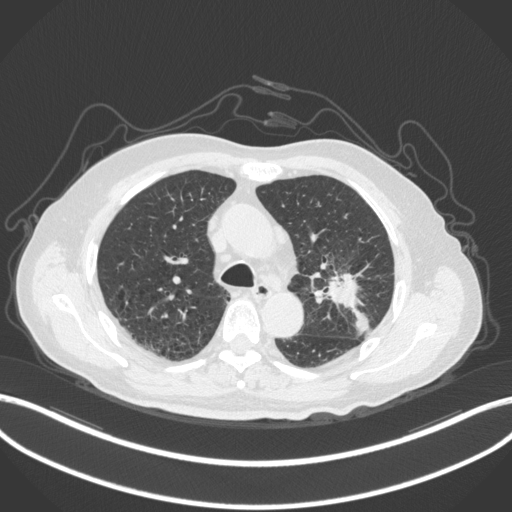
Chest CT, one axial slice; slice 195 of 331 in the series (ordered by position); reconstruction kernel B31f; lung window (W 1500 / L -600 HU); 512 × 512 image matrix, field of view 400 × 400 mm. Patient: male, 79 years. Case-level facts recorded for this patient, not image findings: clinical TNM (as recorded): T2a N1 M1; histopathological grade: G3.
Outlined on this slice (rectangle marked by the reading radiologist):
- lung tumour (recorded histology: adenocarcinoma): bounding box [x1, y1, x2, y2] px = [322, 271, 376, 345]